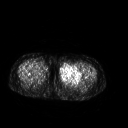
FDG PET of an extremity soft-tissue mass (from a PET/CT study), one axial slice; slice 238 of 267 in the series (ordered by position); 3.27 mm slice thickness; 128 × 128 image matrix, field of view 500 × 500 mm. Patient: female, 42 years. Case-level facts recorded for this patient, not image findings: histological type: pleiomorphic leiomyosarcoma; grade: intermediate; site of the primary tumour: left thigh.
Outlined on this slice (expert contour drawn on MRI and transferred to this co-registered scan by the dataset authors):
- gross tumour volume including surrounding oedema: bounding box <59,64,82,83> (left, top, right, bottom; pixels)
- gross tumour volume (mass): <59,64,82,83>